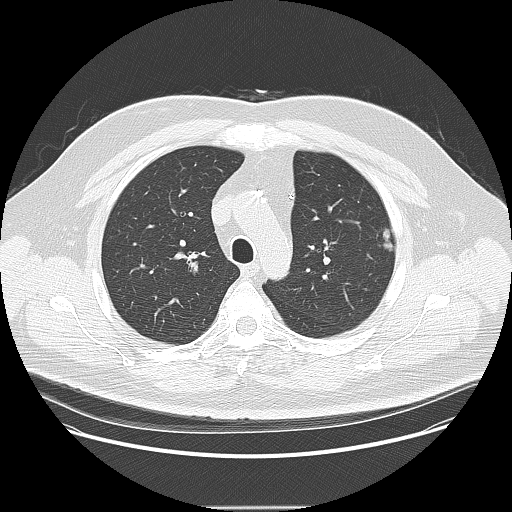
Low-dose screening chest CT, one axial slice. Slice 111 of 157 in the series (ordered by position). Reconstruction kernel LUNG. 120 kVp. Lung window (W 1500 / L -600 HU). 2.5 mm slice thickness. 512 × 512 image matrix.
Annotated regions visible in this slice (manually delineated by an expert):
- lesion 1 (tumor, upper lobe of left lung): box from (x=383, y=229) to (x=394, y=251) px